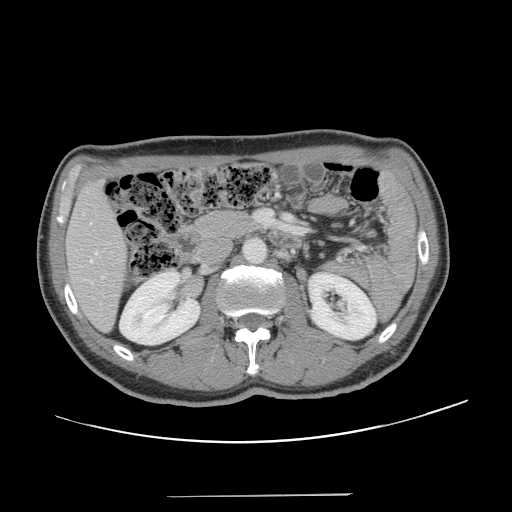
Contrast-enhanced abdominal CT, one axial slice; position 60 of 131 along the scan axis; intravenous contrast given; soft-tissue window (W 400 / L 40 HU); 2.5 mm slice thickness; 512 × 512 image matrix, field of view 403 × 403 mm. Male patient, age 60 years. From the clinical record (not read from this slice): diagnosis: colorectal cancer liver metastases, imaged before liver resection.
Annotated regions visible in this slice (expert manual segmentation):
- hepatic veins: bounding box <90,252,98,263> (left, top, right, bottom; pixels)
- liver: <67,183,125,330>
- planned liver remnant (the part of the liver to remain after resection): <67,183,125,330>